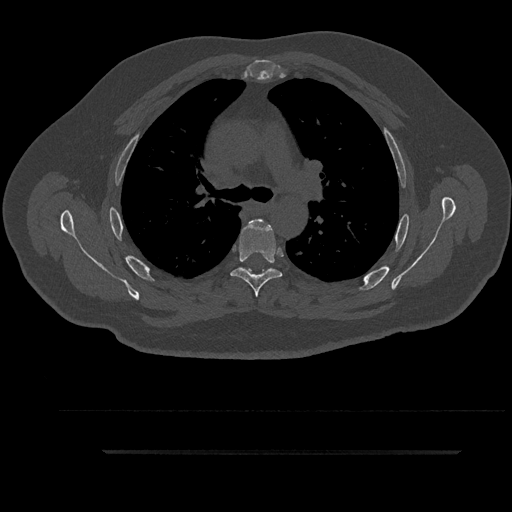
CT including the spine, one axial slice. Slice 628 of 797 in the series (ordered by position). Bone window (W 1800 / L 400 HU). 0.5 mm slice thickness. 512 × 512 image matrix, field of view 432 × 432 mm. Patient: male, 63 years. From the clinical record (not read from this slice): primary cancer: renal; vertebrae with lytic lesions (as recorded): T8.
Structures marked on this image (semi-automatic segmentation, software-assisted and operator-edited):
- T4 vertebra: bounding box <248,219,263,225> (left, top, right, bottom; pixels)
- T5 vertebra: <231,220,282,298>
- T6 vertebra: <244,268,273,275>